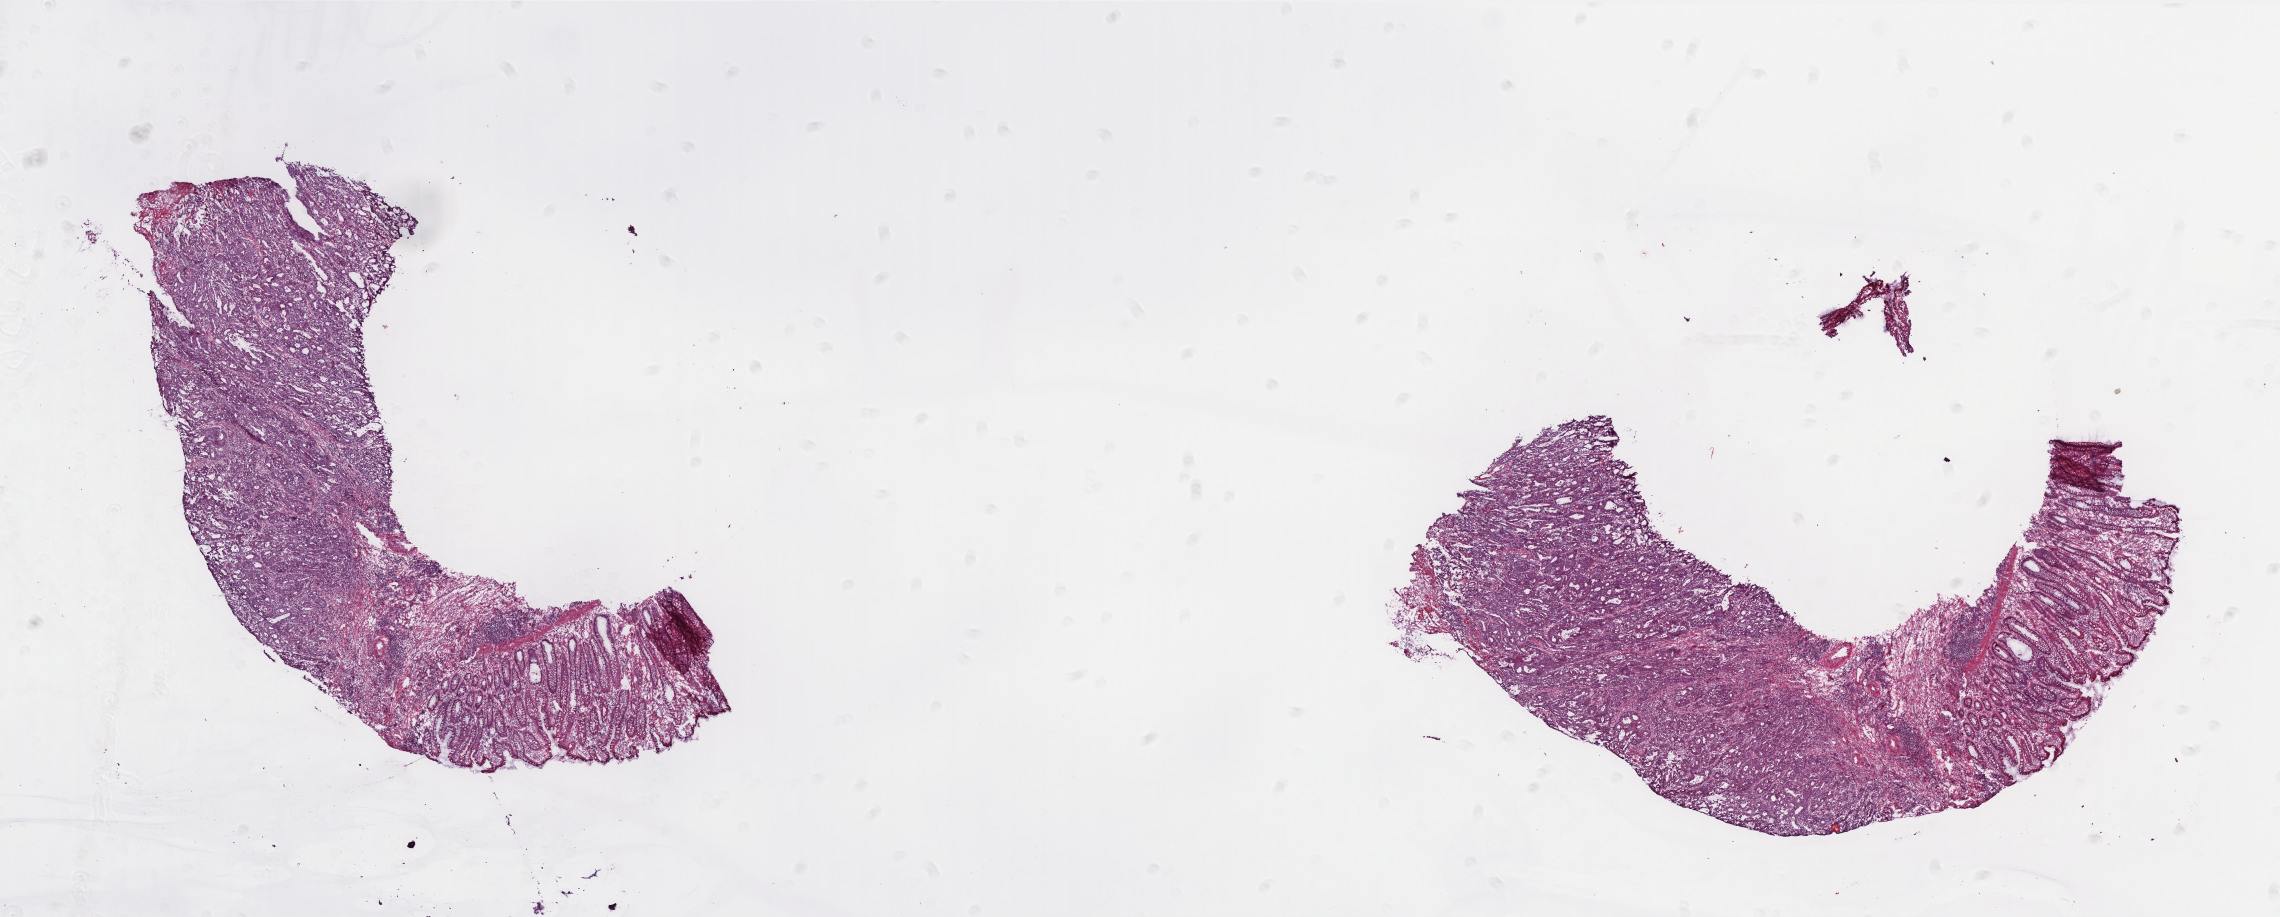
Hematoxylin and eosin (H&E) stained whole-slide image, low-resolution overview of the scanned area, about 18.3 x 7.4 mm (acquisition: 40x scan), frozen section, sample: primary tumour, colon. Patient: male, age at initial diagnosis 64 years. Slide review estimates, as recorded: tumour cells 65%, tumour nuclei 70%.
Histologic diagnosis: Adenocarcinoma, NOS.